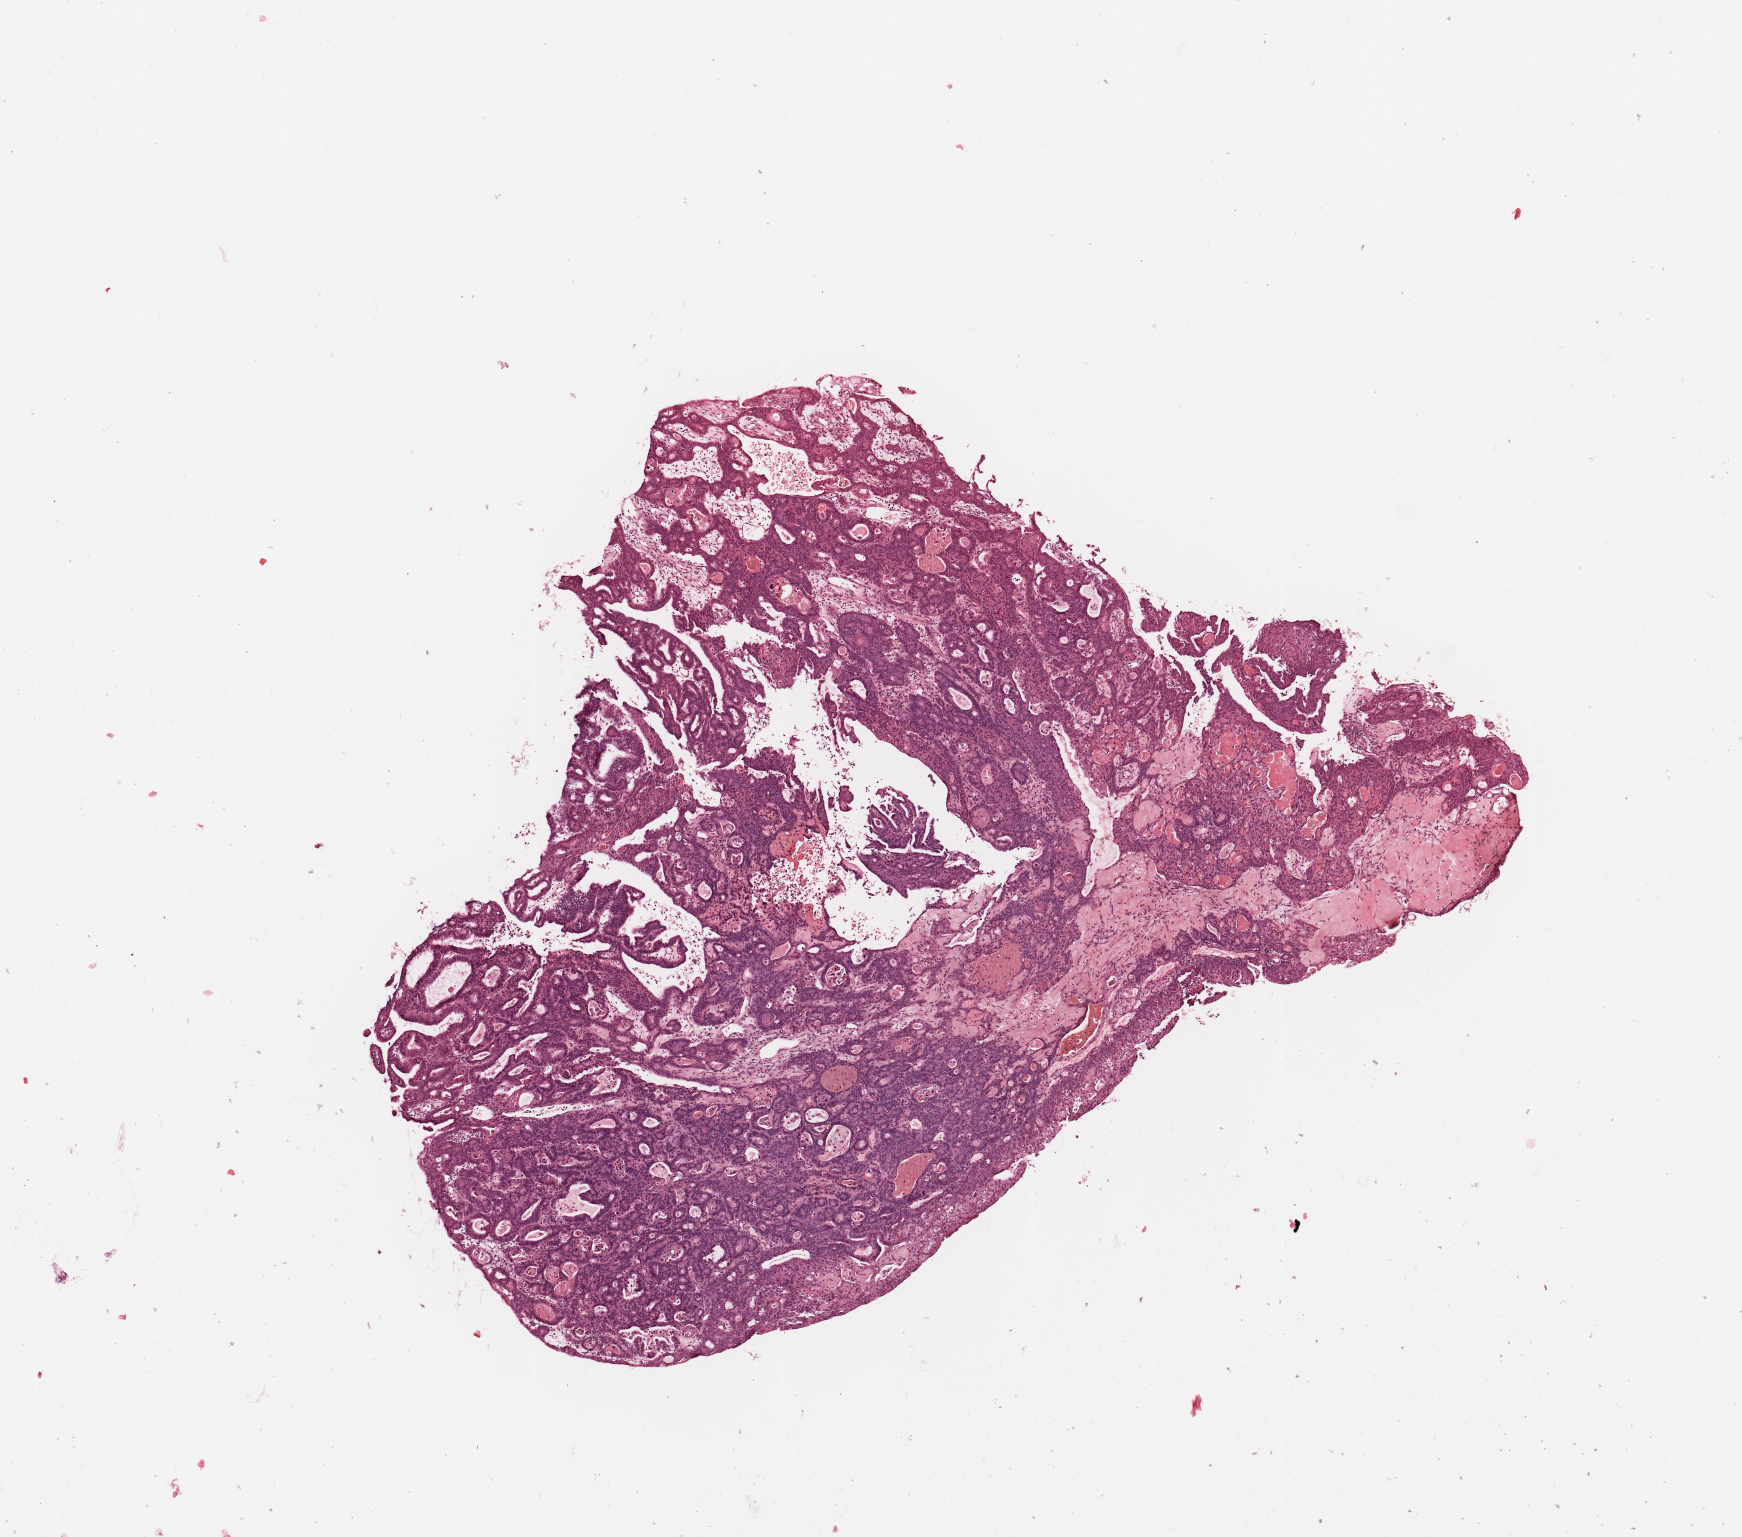
Digitized H&E-stained tissue section (whole slide), shown as a low-resolution overview of the whole scanned area (about 6.9 x 6.1 mm, acquisition: 20x scan). Tumour tissue sample, sampled site: uterus. 68-year-old female patient. Histologic grade: G2 (moderately differentiated). Composition of this section per pathologist review: tumour nuclei 90%, necrosis 3%.
Diagnosis: Endometrioid adenocarcinoma, NOS. AJCC pathologic stage: I. Primary tumour site (as recorded): anterior endometrium.